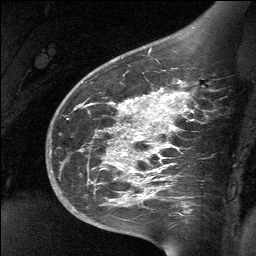
Breast MRI (dynamic contrast-enhanced), one sagittal slice. Position 44 of 64 along the scan axis. Dynamic contrast-enhanced study with each time point stored as its own series, time point 2 of 3 at this slice position (early post-contrast, ordered by acquisition time). 1.5 T. TE 4.8 ms, TR 27 ms. 256 × 256 image matrix, field of view 200 × 200 mm. Female patient, age 39 years. Case-level facts recorded for this patient, not image findings: setting: breast cancer imaged before/during neoadjuvant chemotherapy; receptor status: HER2-positive.
Outlined on this slice (semi-automatic segmentation, software-assisted and operator-edited):
- analysis volume of interest (the breast-tissue region the enhancement analysis was run in; not a lesion): bounding box <70,69,201,224> (left, top, right, bottom; pixels)
- tumour enhancement mask (voxels above the 90 % enhancement threshold inside the analysis volume of interest): <118,93,186,178>